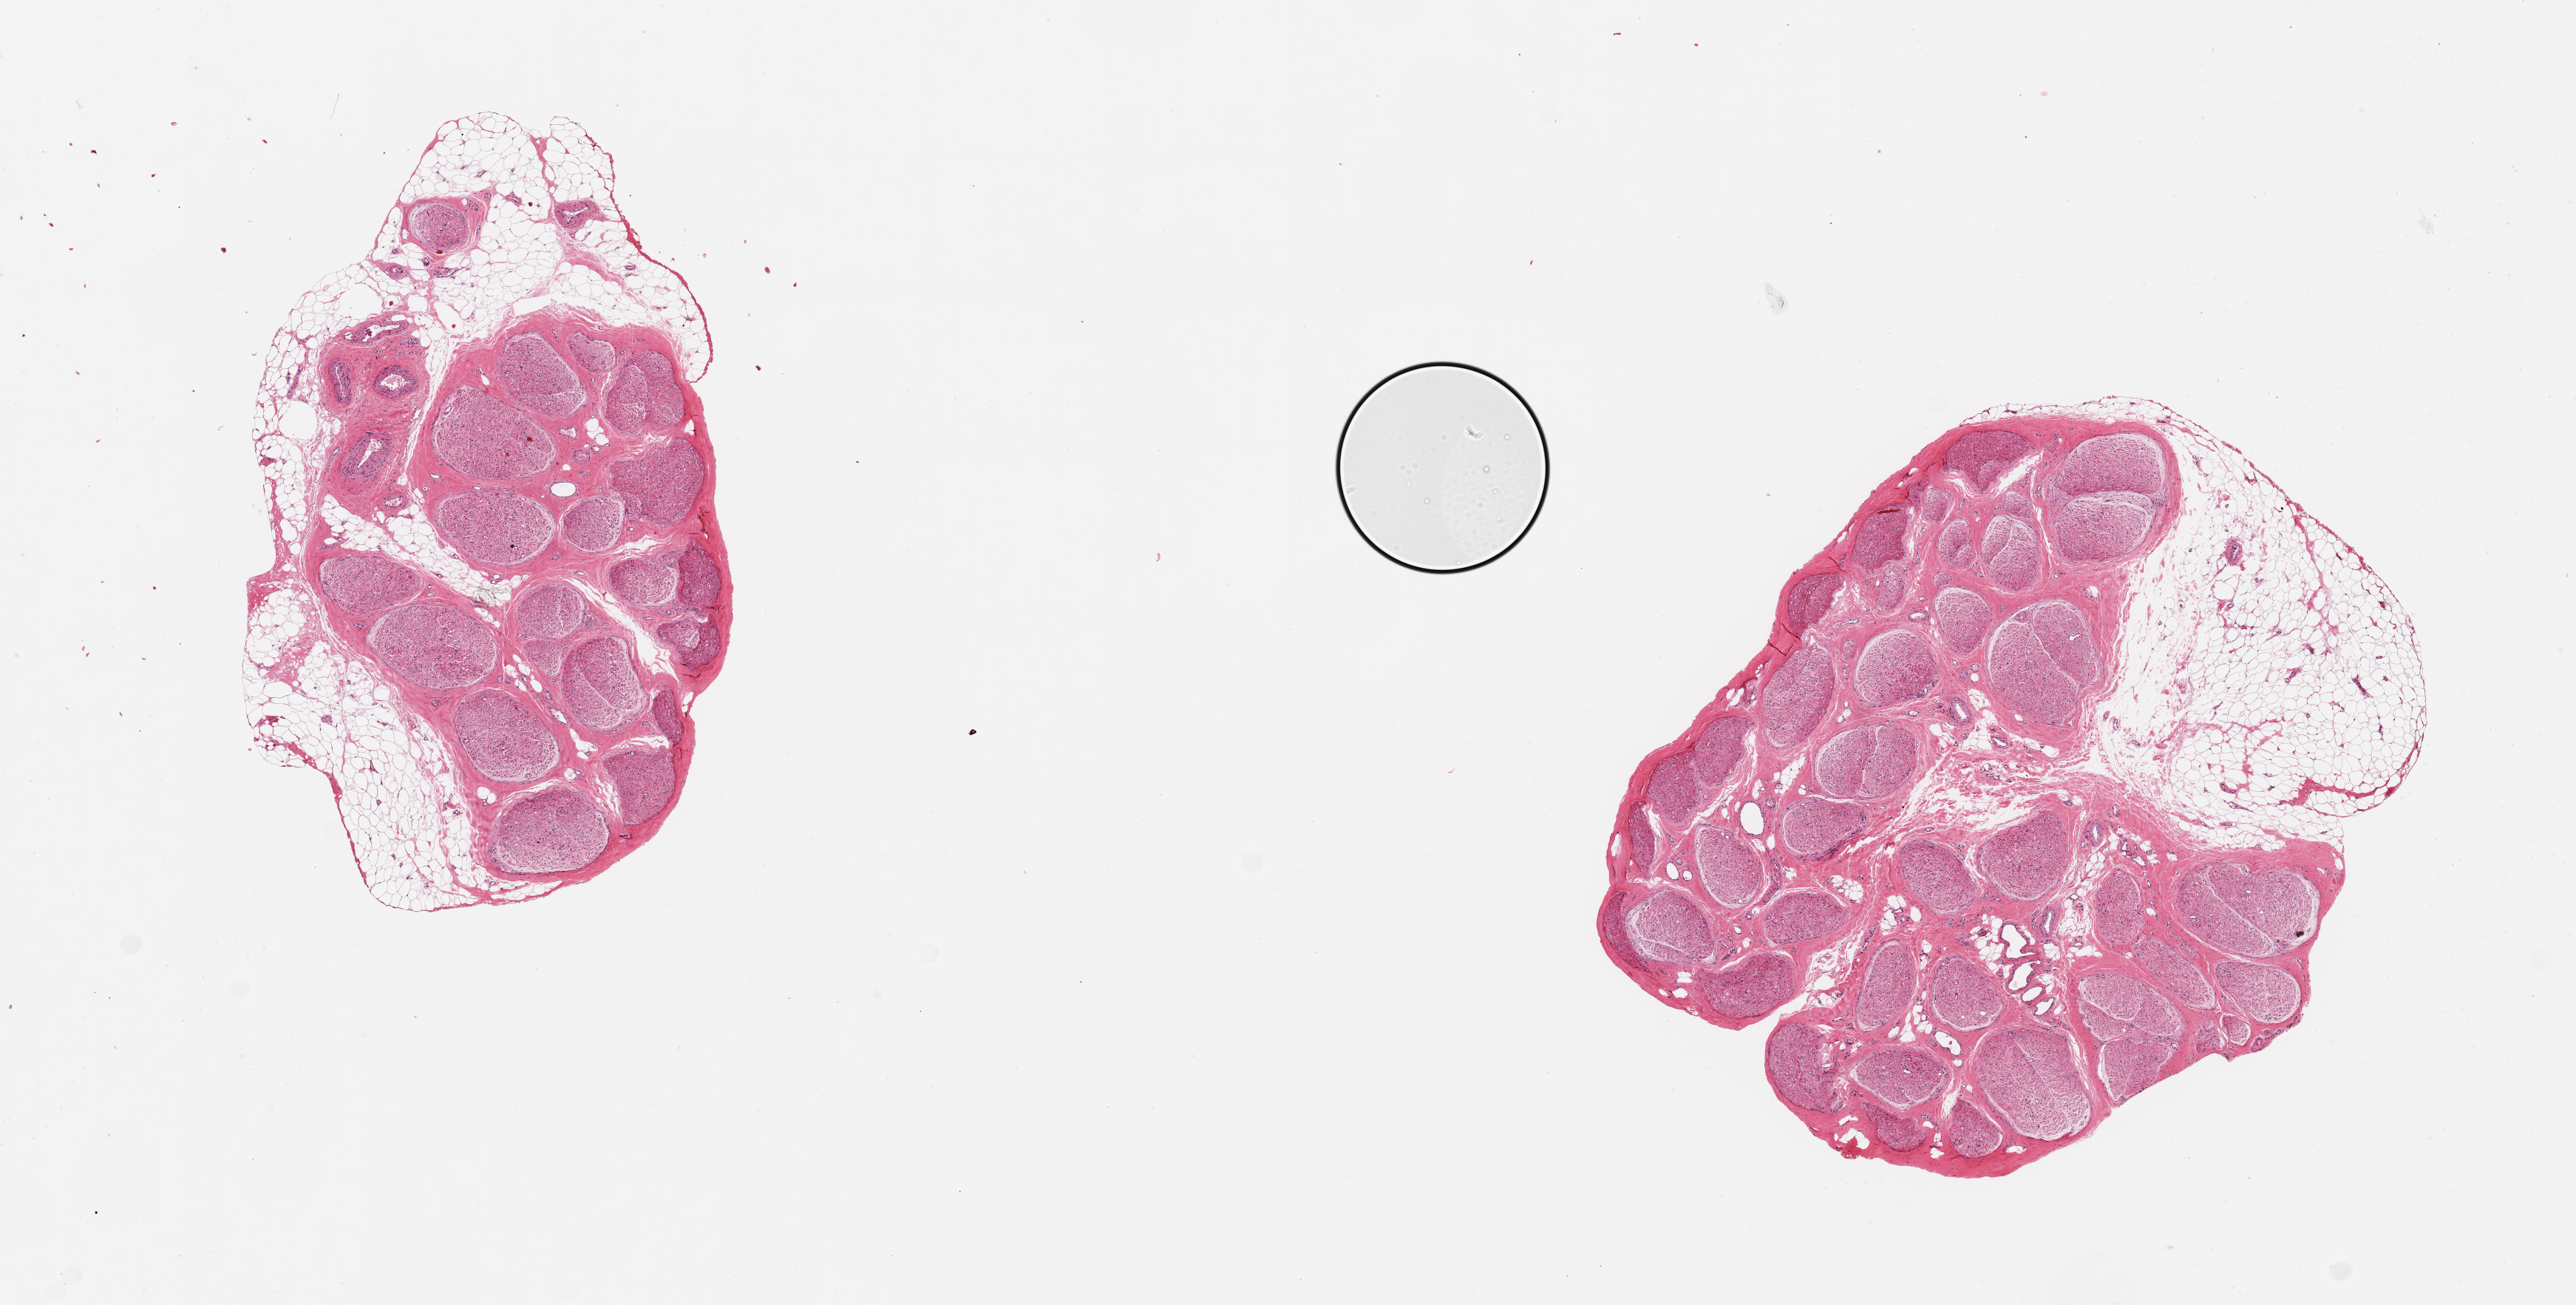
Haematoxylin and eosin whole-slide image, brightfield — a low-resolution overview of the entire scanned area, about 13.8 x 7.0 mm. PAXgene-fixed, paraffin-embedded tissue. Target tissue: tibial nerve. Tissue donor sample. Female donor.
* reviewer comment on this tissue sample: 2 pieces ~3mm d; Adherent discontinuous fat on both up to1.5mm